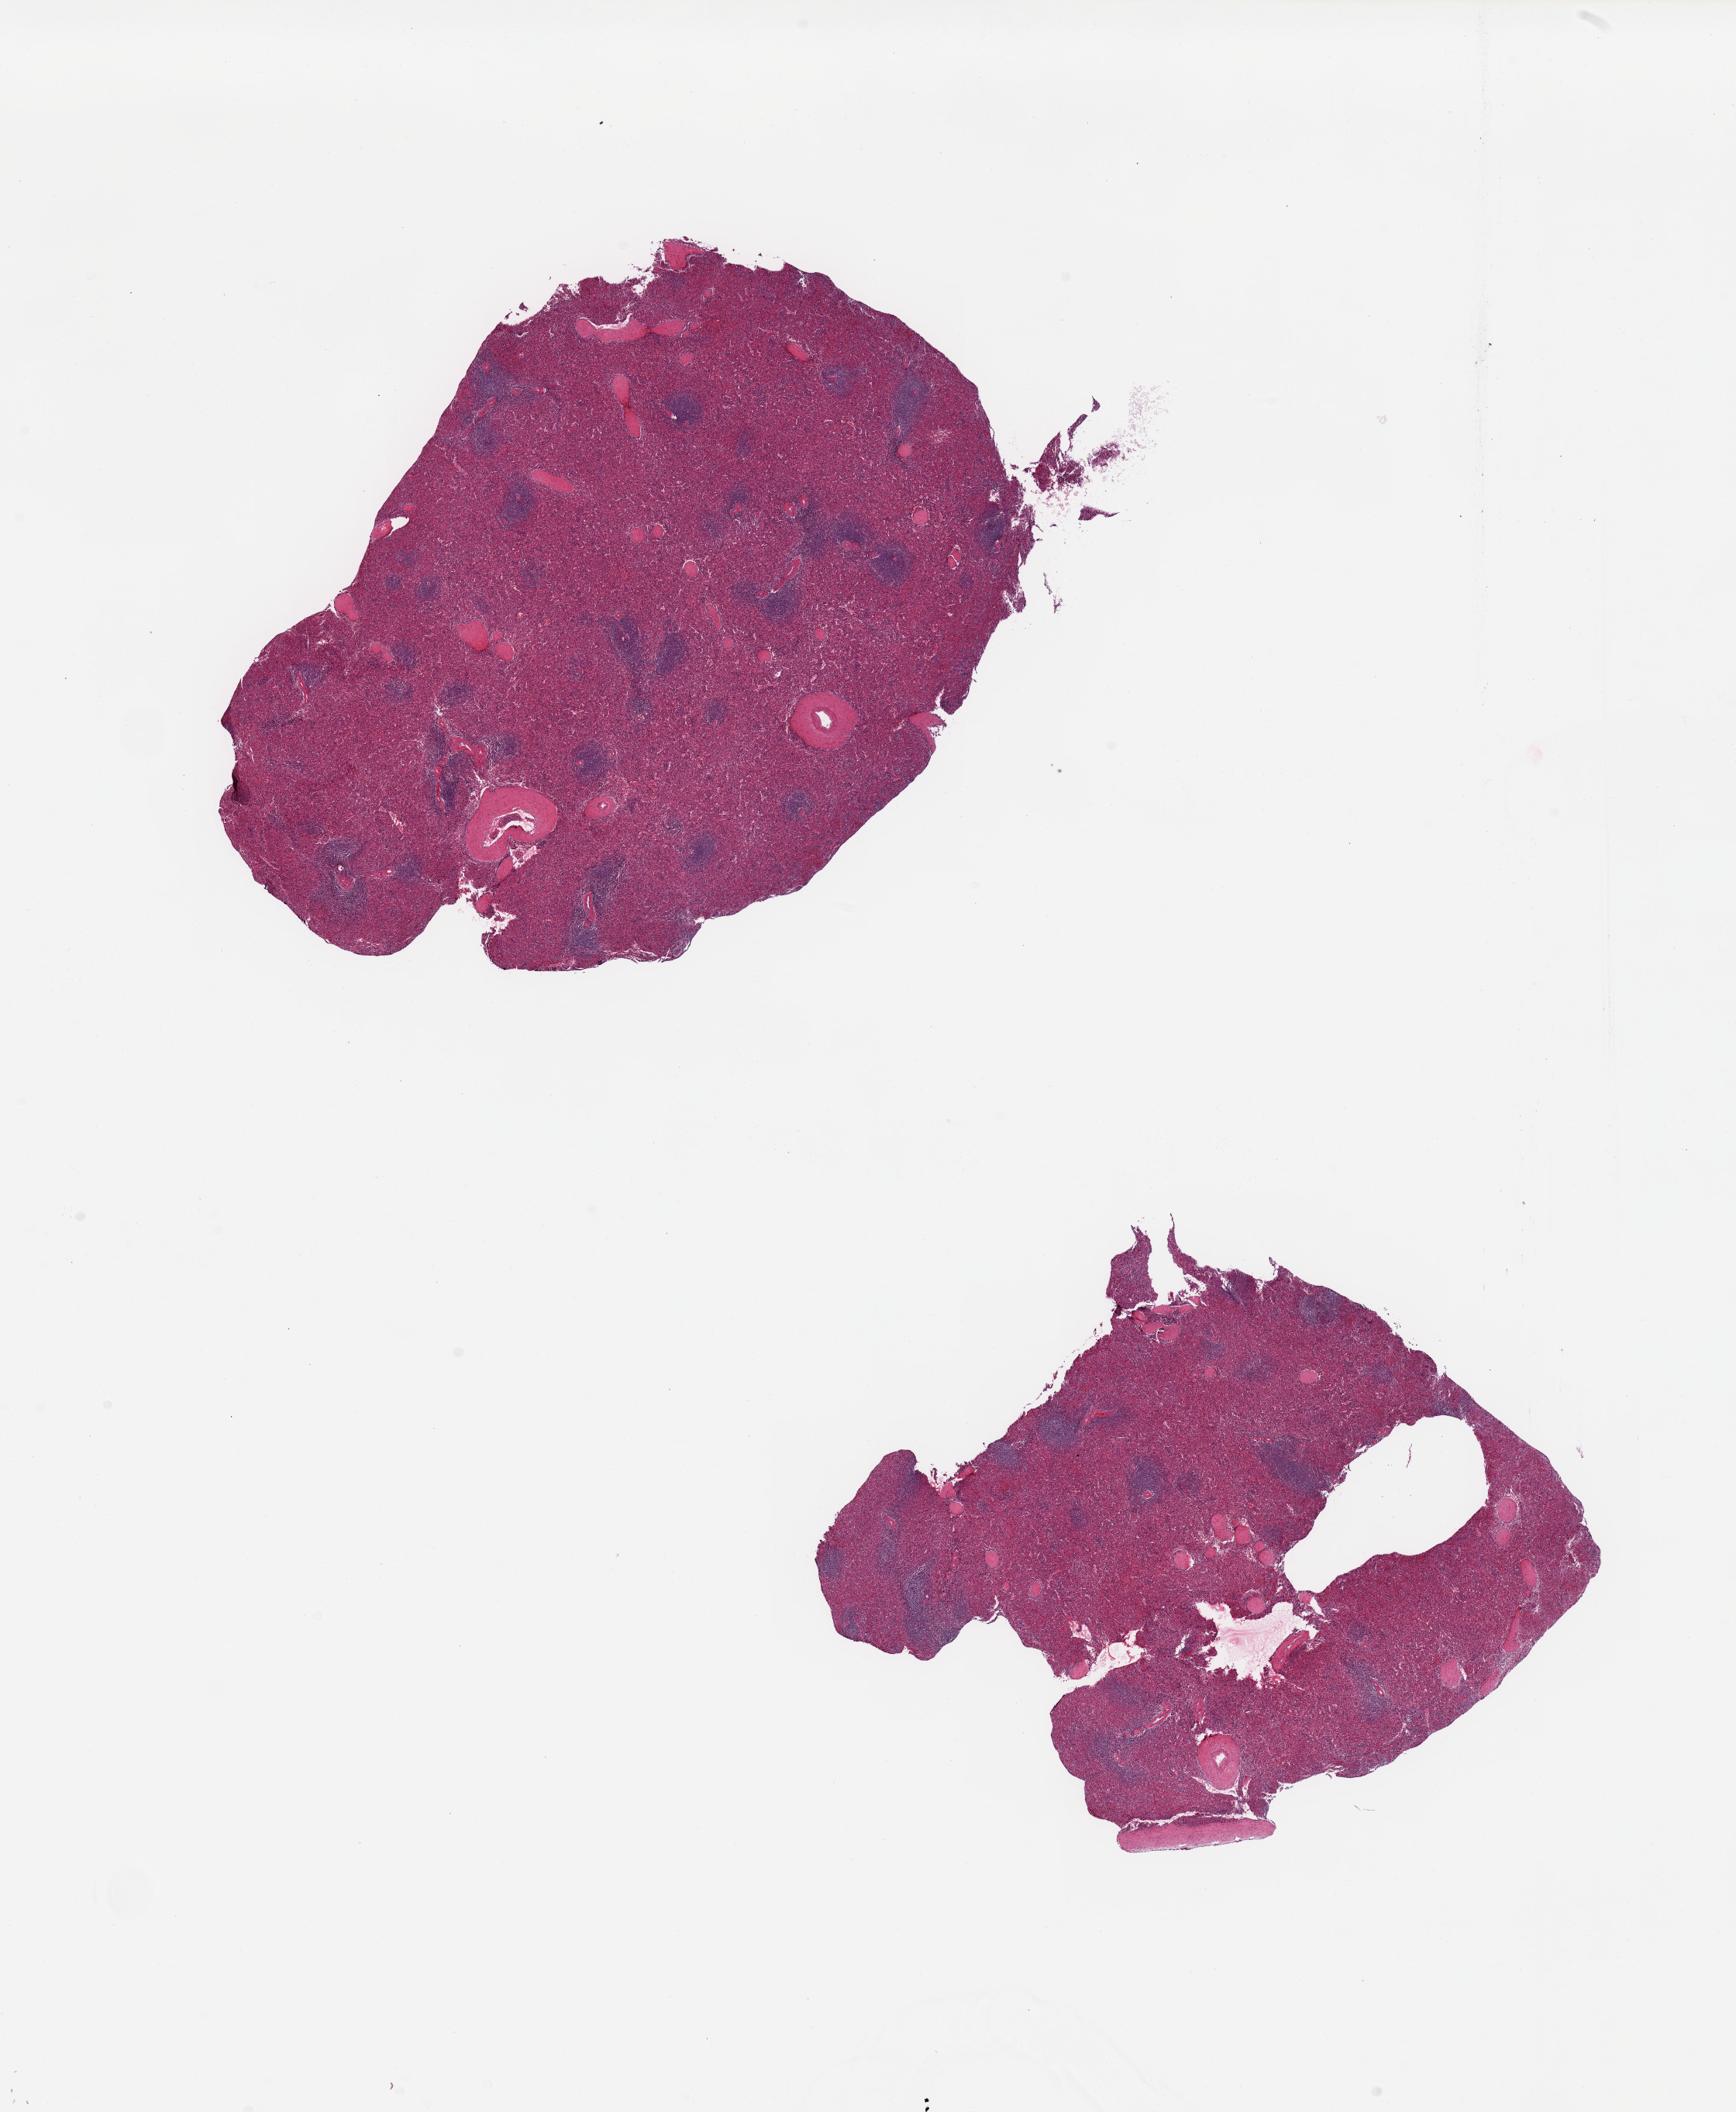
Digitized haematoxylin and eosin-stained section — a low-resolution overview of the entire scanned area, about 17.7 x 21.6 mm. PAXgene-fixed, paraffin-embedded tissue. Sampled site (target tissue): spleen. Tissue donor sample.
Pathologist's review note for this sample: 2 pieces; congestion.